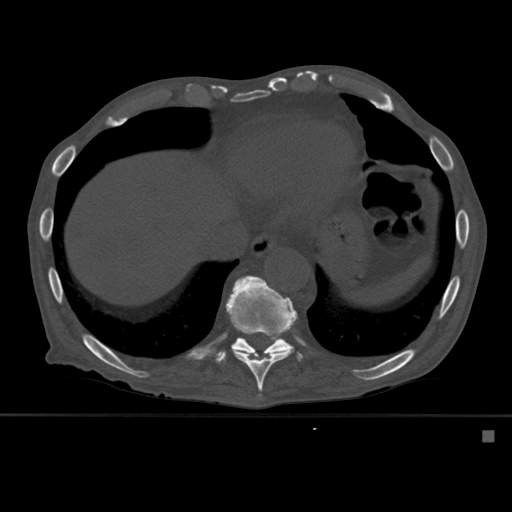
CT including the spine, one axial slice. Bone window (W 1800 / L 400 HU). 1.5 mm slice thickness. 512 × 512 image matrix, field of view 373 × 373 mm. Male patient, age 78 years. Case-level facts recorded for this patient, not image findings: primary cancer: prostate.
Outlined on this slice (semi-automatically segmented with operator editing):
- T10 vertebra: bounding box (x1, y1, x2, y2) in pixels: (225, 275, 297, 399)
- T11 vertebra: (216, 292, 300, 364)